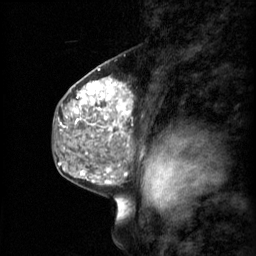
Breast MRI (dynamic contrast-enhanced), one sagittal slice; slice 34 of 60 in the series (ordered by position); 3 images stored at this slice position (order not interpretable as contrast timing); 1.5 T; TE 4.2 ms, TR 11 ms; 2 mm slice thickness; 256 × 256 image matrix, field of view 200 × 200 mm. Female patient, age 48 years.
Annotated regions visible in this slice (semi-automatically segmented with operator editing):
- analysis volume of interest (the breast-tissue region the enhancement analysis was run in; not a lesion): bounding box [x1, y1, x2, y2] px = [69, 74, 133, 147]
- tumour enhancement mask (voxels above the 70 % enhancement threshold inside the analysis volume of interest): [78, 78, 133, 147]